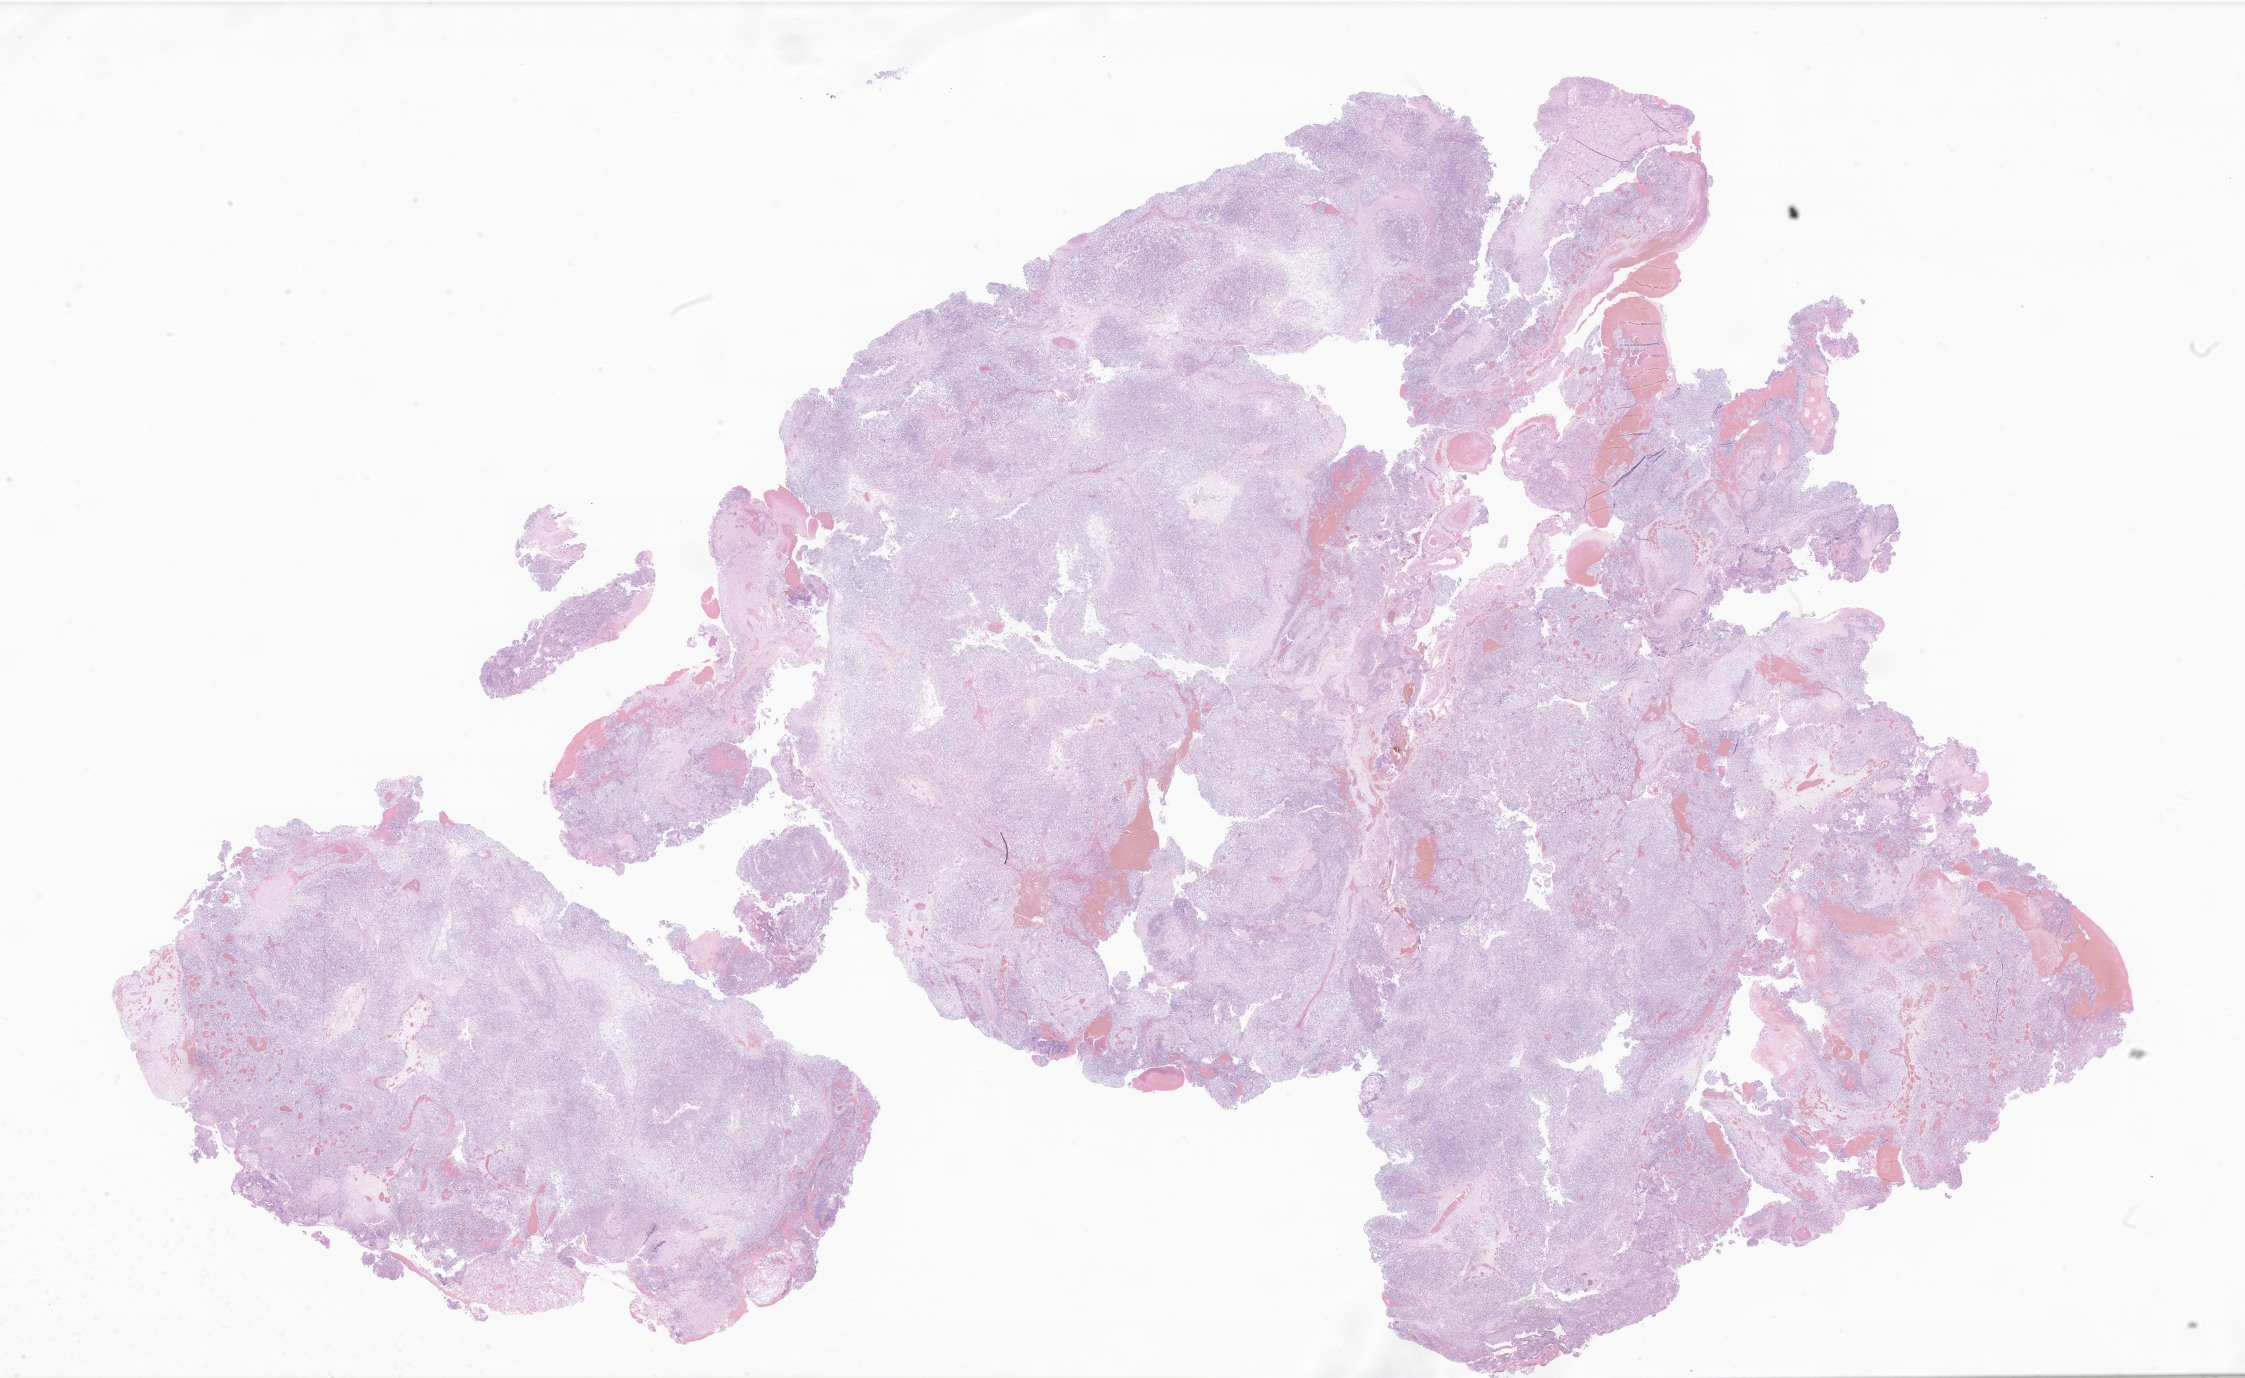
Digitized haematoxylin and eosin-stained section of tumor tissue from the brain, a low-resolution overview of the entire scanned area, about 37.9 x 23.2 mm; formalin-fixed paraffin-embedded section. Patient: male, age 218 days.
* diagnosis: Neoplasm, malignant